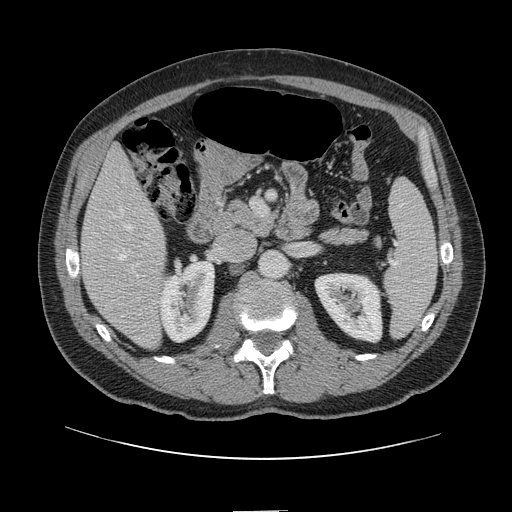
Contrast-enhanced abdominal CT, one axial slice. Intravenous contrast given. Soft-tissue window (W 400 / L 40 HU). 2.5 mm slice thickness. 512 × 512 image matrix, field of view 412 × 412 mm. Male patient, age 66 years. Case-level facts recorded for this patient, not image findings: diagnosis: colorectal cancer liver metastases, imaged before liver resection; multiple liver metastases: no; largest metastasis: 3.5 cm; disease in both lobes: no.
Annotated regions visible in this slice (expert manual segmentation):
- hepatic veins: bounding box [x1, y1, x2, y2] px = [120, 209, 132, 260]
- liver: [82, 149, 165, 348]
- planned liver remnant (the part of the liver to remain after resection): [81, 150, 160, 275]